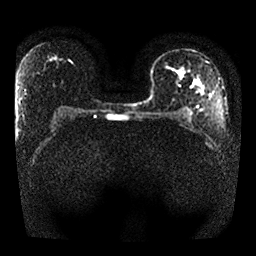
Breast MRI, one axial slice. Position 15 of 25 along the scan axis. Diffusion-weighted series; image 2 of 4 stored at this slice position (different b-values; order by instance number). 1.5 T. 256 × 256 image matrix. Female patient.
Structures marked on this image (expert manual segmentation):
- tumour on diffusion-weighted imaging: box from (x=177, y=68) to (x=184, y=80) px